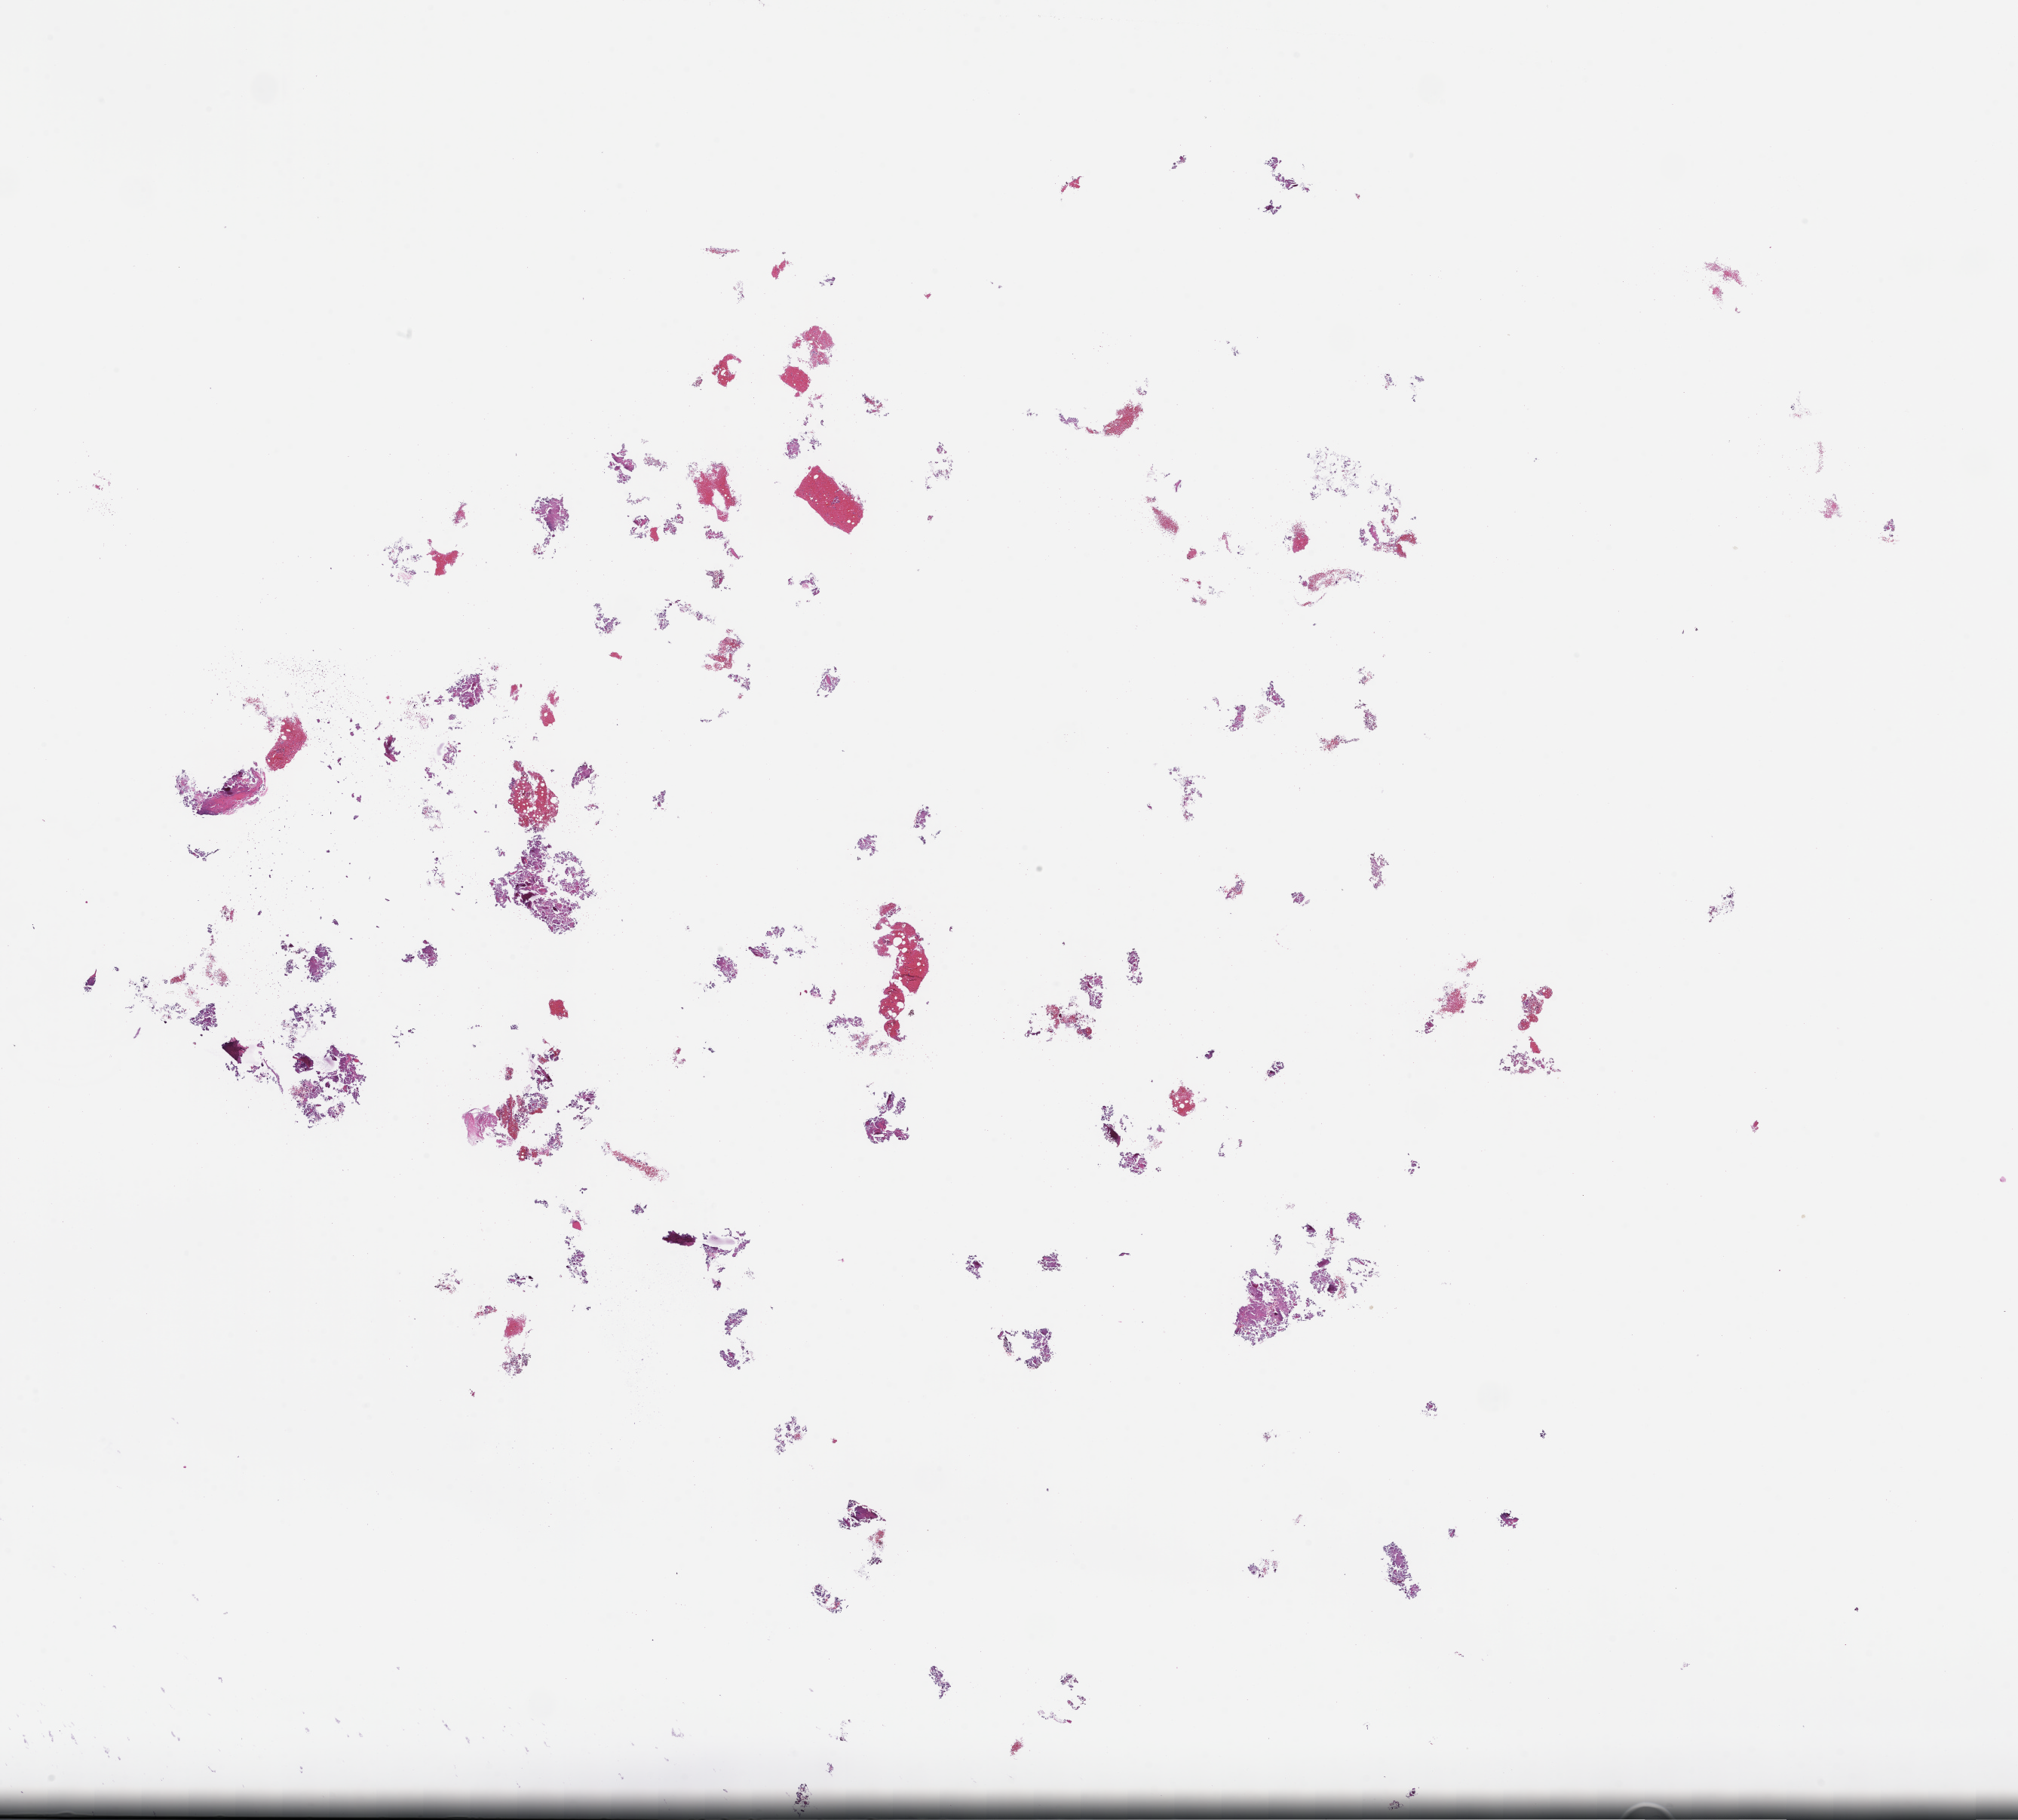
Haematoxylin and eosin whole-slide image — a low-resolution overview of the entire scanned area, about 21.6 x 19.5 mm, formalin-fixed, paraffin-embedded (FFPE) tissue. Patient sex: male.
This section: metastatic tumor tissue. Primary diagnosis of the patient: Prostate Carcinoma.